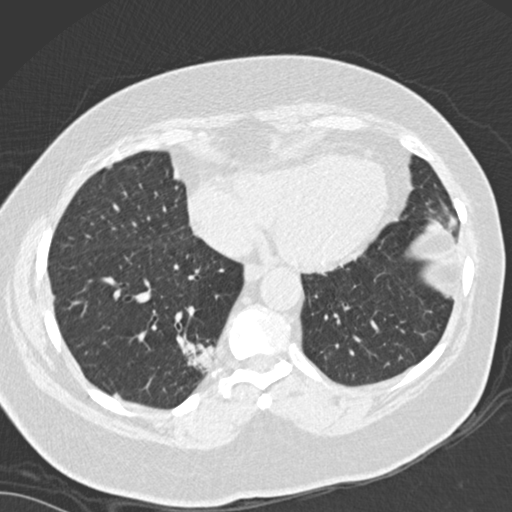
Axial slice from a low-dose chest CT screening exam. First (baseline) screen. Lung window (W 1500 / L -600 HU). 2 mm slice thickness. Standard (soft-tissue) reconstruction kernel (B30f). 120 kVp. Female, age 66 years at enrolment. Current smoker at enrolment.
Expert-annotated lung lesion, bounding box [x1, y1, x2, y2] px = [142, 311, 237, 410]. The screening reader recorded 3 non-calcified nodules or masses ≥4 mm on this exam (left lower lobe, left lower lobe, right lower lobe); which of them this box marks is not recorded. Lung cancer was diagnosed 67 days after this screen: adenocarcinoma, NOS, right lower lobe, well differentiated (G1), stage IB (AJCC 6th edition), 55 mm at pathology.